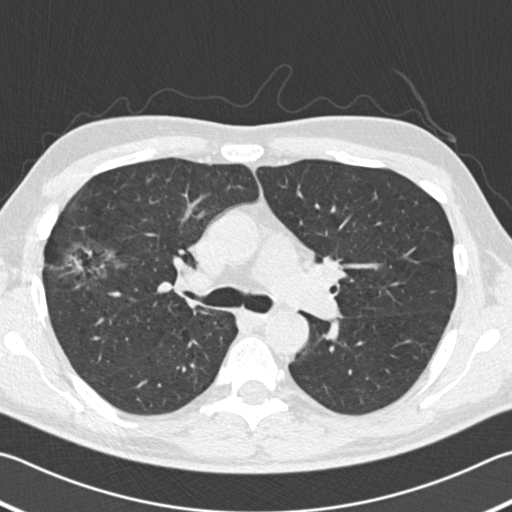
Low-dose screening chest CT, one axial slice. 120 kVp. Lung window (W 1500 / L -600 HU). 2 mm slice thickness. 512 × 512 image matrix, field of view 344 × 344 mm.
Annotated regions visible in this slice (manually delineated by an expert):
- lesion 1 (tumor, upper lobe of right lung): bounding box [x1, y1, x2, y2] px = [66, 242, 120, 279]